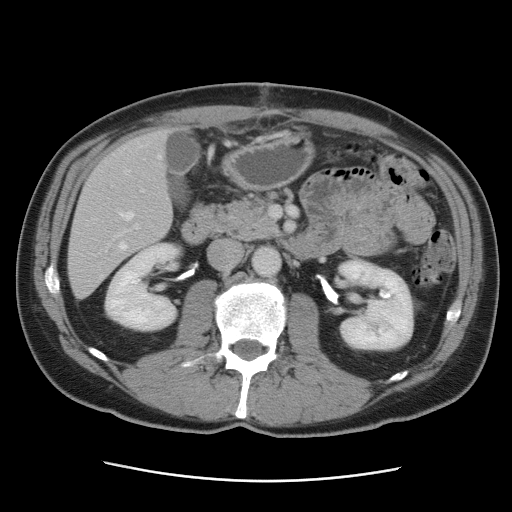
Contrast-enhanced abdominal CT, one axial slice; position 36 of 89 along the scan axis; soft-tissue window (W 400 / L 40 HU); 5 mm slice thickness; 512 × 512 image matrix, field of view 366 × 366 mm. Male patient, age 59 years. From the clinical record (not read from this slice): diagnosis: colorectal cancer liver metastases, imaged before liver resection; multiple liver metastases: yes; largest metastasis: 0.6 cm.
Annotated regions visible in this slice (manually delineated by an expert):
- hepatic veins: bounding box [x1, y1, x2, y2] px = [100, 155, 162, 278]
- liver: [69, 130, 172, 298]
- planned liver remnant (the part of the liver to remain after resection): [74, 129, 173, 245]
- portal vein (with intrahepatic branches): [116, 189, 144, 237]